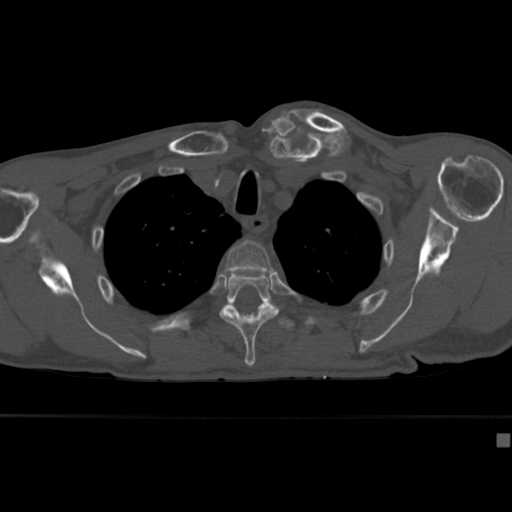
CT including the spine, one axial slice. Position 322 of 430 along the scan axis. Reconstruction kernel Br40s. 120 kVp. Bone window (W 1800 / L 400 HU). 512 × 512 image matrix, field of view 337 × 337 mm. Patient: male, 64 years. Case-level facts recorded for this patient, not image findings: primary cancer: uterus; vertebrae with lytic lesions (as recorded): T1, T4, T5, T7, L5.
Annotated regions visible in this slice (semi-automatic segmentation, software-assisted and operator-edited):
- T3 vertebra: bounding box <223,240,275,275> (left, top, right, bottom; pixels)
- T4 vertebra: <219,272,286,367>
- T5 vertebra: <279,319,295,329>